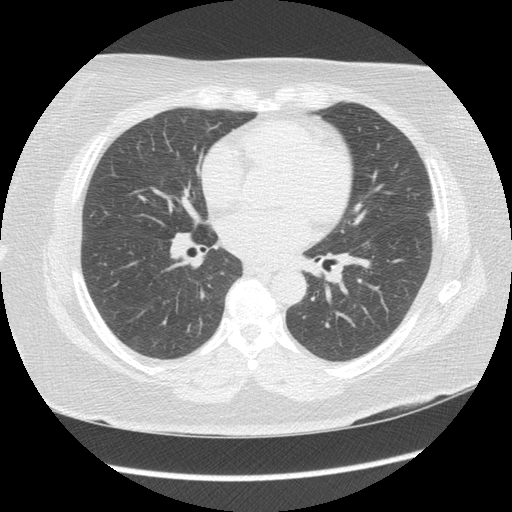
Low-dose screening chest CT, one axial slice. Slice 68 of 144 in the series (ordered by position). Reconstruction kernel STANDARD. 120 kVp. Lung window (W 1500 / L -600 HU). 2.5 mm slice thickness. 512 × 512 image matrix.
Annotated regions visible in this slice (manually delineated by an expert):
- lesion 1 (tumor, lower lobe of left lung): bounding box [x1, y1, x2, y2] px = [362, 241, 370, 248]